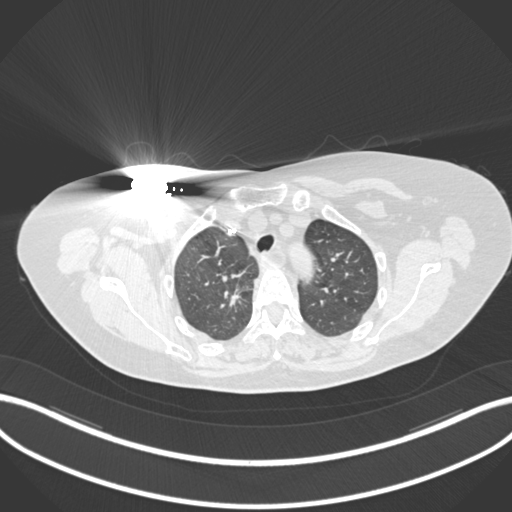
Chest CT, one axial slice; slice 144 of 176 in the series (ordered by position); reconstruction kernel B30f; lung window (W 1500 / L -600 HU); 1 mm slice thickness; 512 × 512 image matrix. Female patient, age 72 years. Case-level facts recorded for this patient, not image findings: clinical TNM (as recorded): T1c N0 M0.
Annotated regions visible in this slice (bounding box drawn by a radiologist):
- lung tumour (recorded histology: adenocarcinoma): bounding box <218,278,251,320> (left, top, right, bottom; pixels)